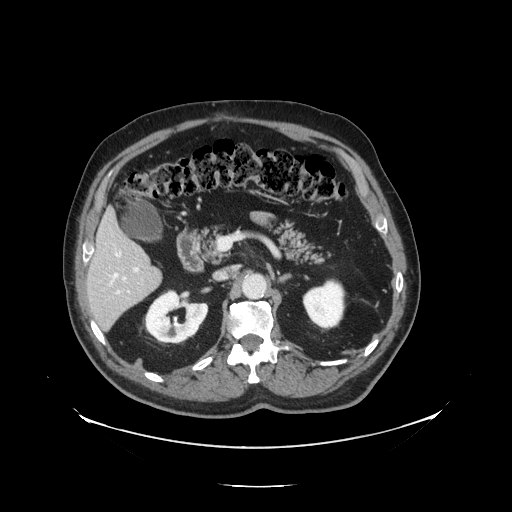
Contrast-enhanced abdominal CT, one axial slice; position 69 of 138 along the scan axis; reconstruction kernel STANDARD; 120 kVp; soft-tissue window (W 400 / L 40 HU); 2.5 mm slice thickness; 512 × 512 image matrix, field of view 497 × 497 mm. Male patient, age 77 years. From the clinical record (not read from this slice): diagnosis: colorectal cancer liver metastases, imaged before liver resection; multiple liver metastases: no; largest metastasis: 1.5 cm; disease in both lobes: no.
Outlined on this slice (expert manual segmentation):
- hepatic veins: bounding box [x1, y1, x2, y2] px = [111, 252, 126, 282]
- liver: [88, 213, 161, 331]
- planned liver remnant (the part of the liver to remain after resection): [88, 213, 152, 286]
- portal vein (with intrahepatic branches): [115, 267, 139, 295]